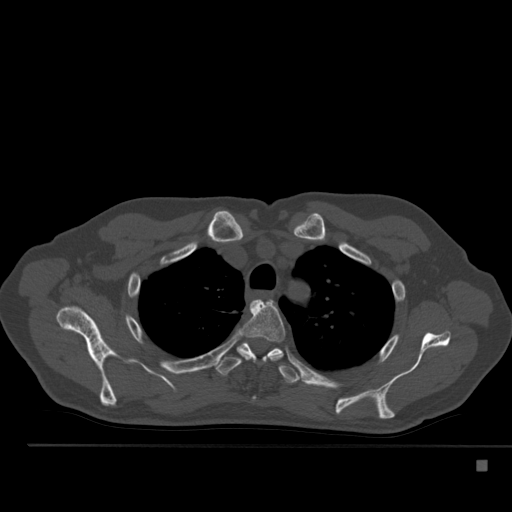
CT including the spine, one axial slice; slice 391 of 517 in the series (ordered by position); reconstruction kernel Br40s; 120 kVp; bone window (W 1800 / L 400 HU); 1.5 mm slice thickness; 512 × 512 image matrix, field of view 408 × 408 mm. Male patient, age 70 years. From the clinical record (not read from this slice): primary cancer: renal; vertebrae with lytic lesions (as recorded): T4, T6, T10, T12, L3, L4, L5.
Structures marked on this image (semi-automatically segmented with operator editing):
- T3 vertebra: box from (x=239, y=300) to (x=286, y=361) px
- T4 vertebra: (x=215, y=341)–(x=300, y=384)